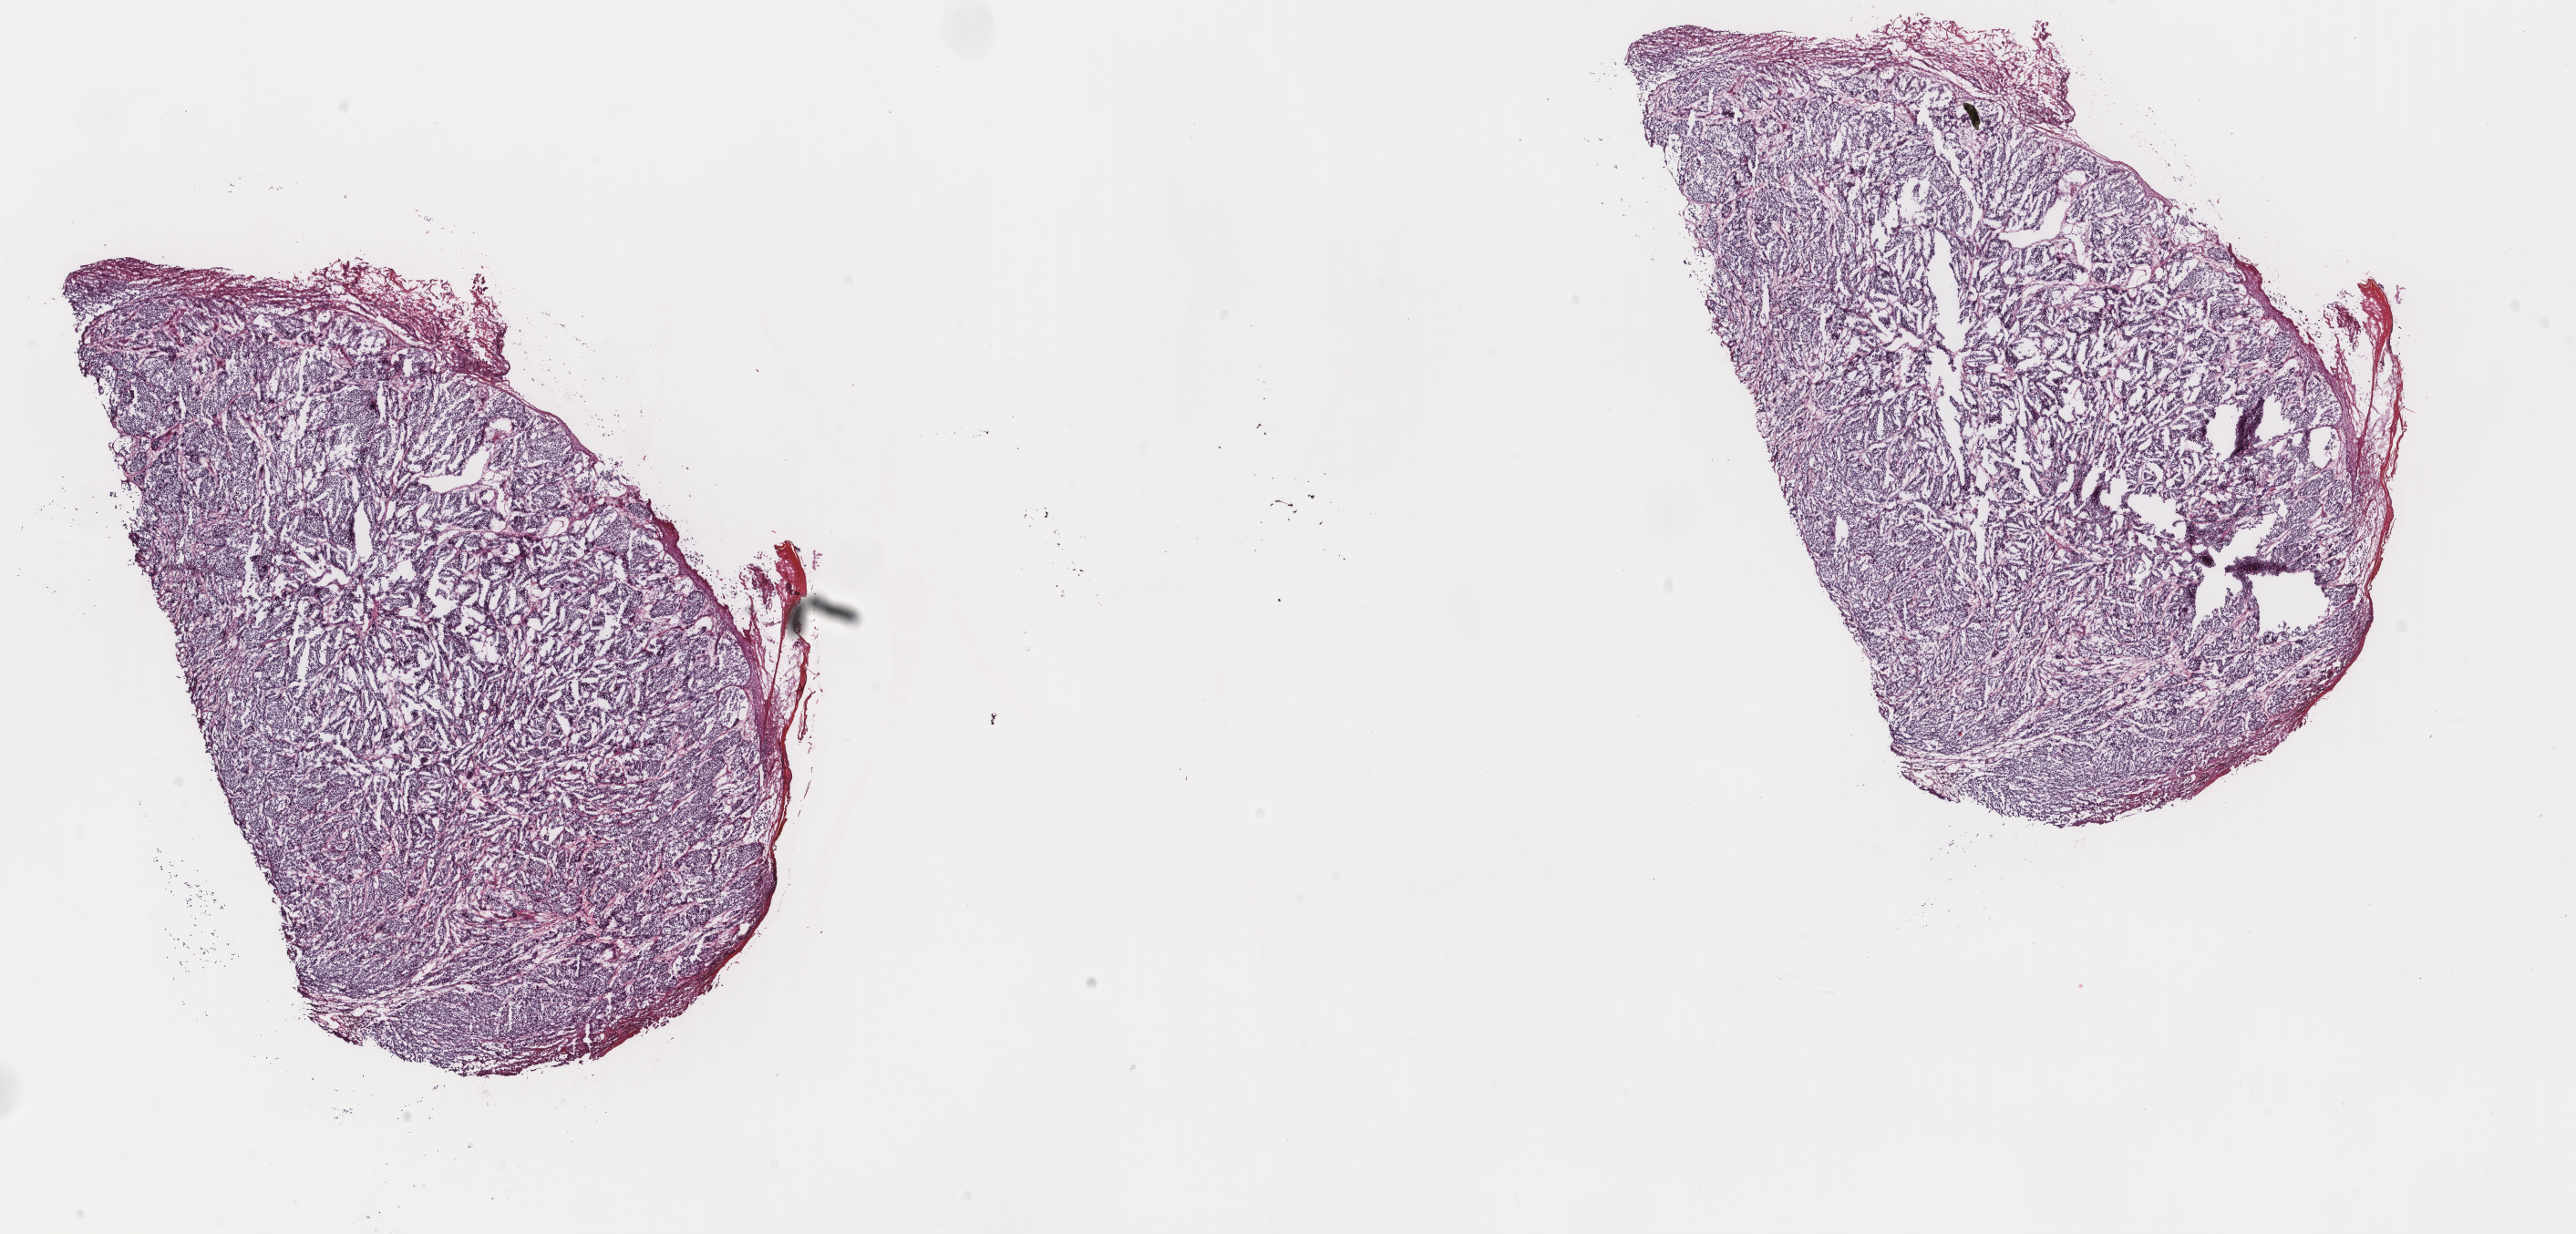
Whole-slide histology image, H&E-stained — low-resolution overview of the scanned area, about 22.4 x 10.7 mm. Frozen section from the top of the tissue portion. Sample: primary tumour, skin. Female, age 58 years at initial diagnosis. Composition of this section per pathologist review: tumour cells 100%, tumour nuclei 80%.
Pathologic diagnosis: Malignant melanoma, NOS.